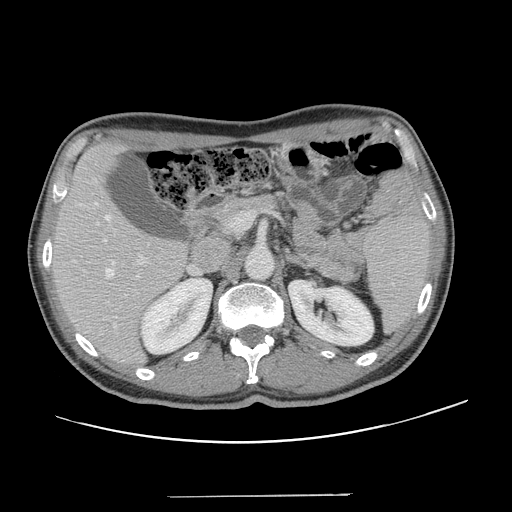
Contrast-enhanced abdominal CT, one axial slice. Slice 78 of 131 in the series (ordered by position). 120 kVp. Intravenous contrast given. Soft-tissue window (W 400 / L 40 HU). 512 × 512 image matrix, field of view 403 × 403 mm. Male patient, age 60 years. Case-level facts recorded for this patient, not image findings: diagnosis: colorectal cancer liver metastases, imaged before liver resection.
Annotated regions visible in this slice (expert manual segmentation):
- hepatic veins: bounding box [x1, y1, x2, y2] px = [96, 203, 139, 277]
- liver: [53, 144, 186, 365]
- planned liver remnant (the part of the liver to remain after resection): [53, 145, 186, 360]